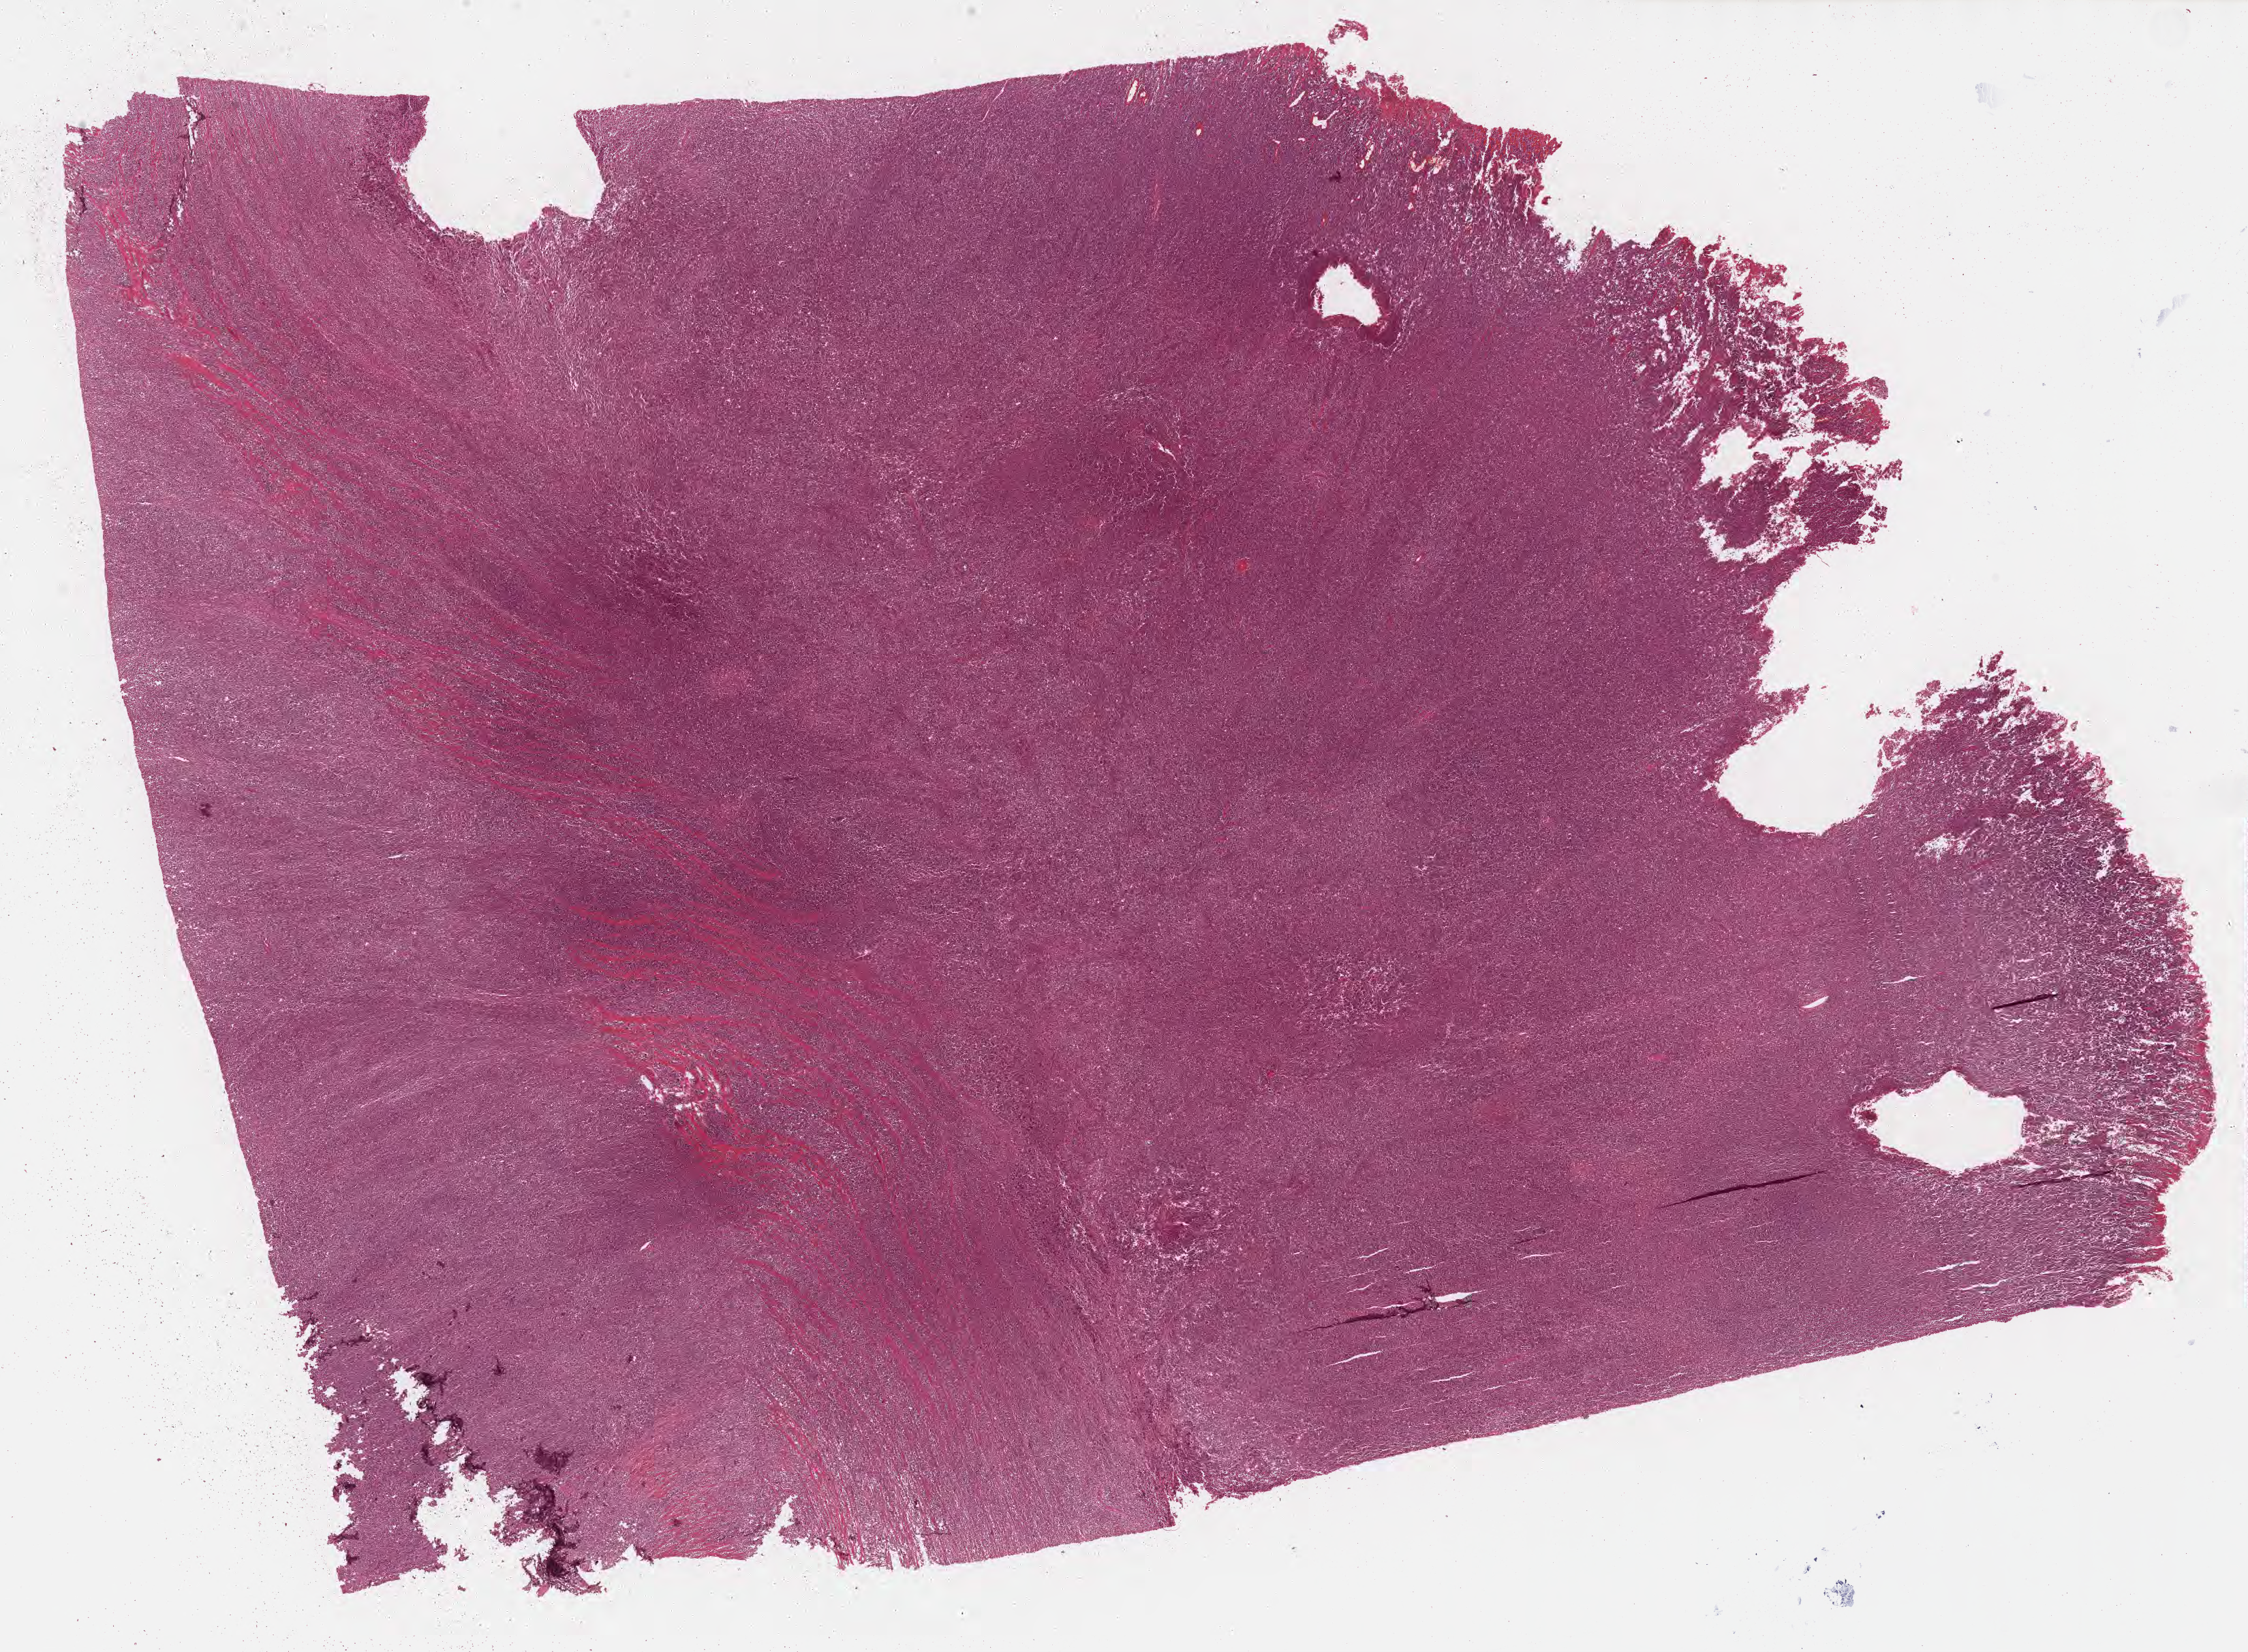
Whole-slide image, H&E stain, low-resolution overview of the scanned area, about 26.7 x 19.6 mm, formalin-fixed paraffin-embedded section, primary tumor. Male patient, 17 years old. Pathologist review of this section (percent, as recorded): tumor cells 90%, tumor nuclei 95%, stromal cells 5%, necrosis 5%, normal cells 0%. Infiltration values recorded for this section: lymphocyte infiltration 80%, monocyte infiltration 10%, neutrophil infiltration 0%.
- histologic diagnosis: Burkitt lymphoma, NOS
- Ann Arbor stage (patient): Stage III
- section: top of the tissue portion